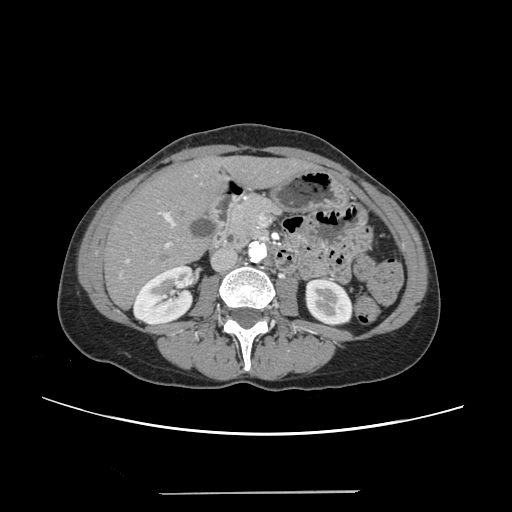
Contrast-enhanced abdominal CT, one axial slice. Slice 98 of 240 in the series (ordered by position). 120 kVp. Intravenous contrast given. Soft-tissue window (W 400 / L 40 HU). 1.25 mm slice thickness. 512 × 512 image matrix, field of view 371 × 371 mm. Female patient, age 60 years. Case-level facts recorded for this patient, not image findings: diagnosis: colorectal cancer liver metastases, imaged before liver resection; multiple liver metastases: no; largest metastasis: 1.5 cm; disease in both lobes: no.
Structures marked on this image (expert manual segmentation):
- liver: bounding box (x1, y1, x2, y2) in pixels: (106, 158, 306, 308)
- planned liver remnant (the part of the liver to remain after resection): (106, 159, 305, 308)
- portal vein (with intrahepatic branches): (124, 174, 197, 263)